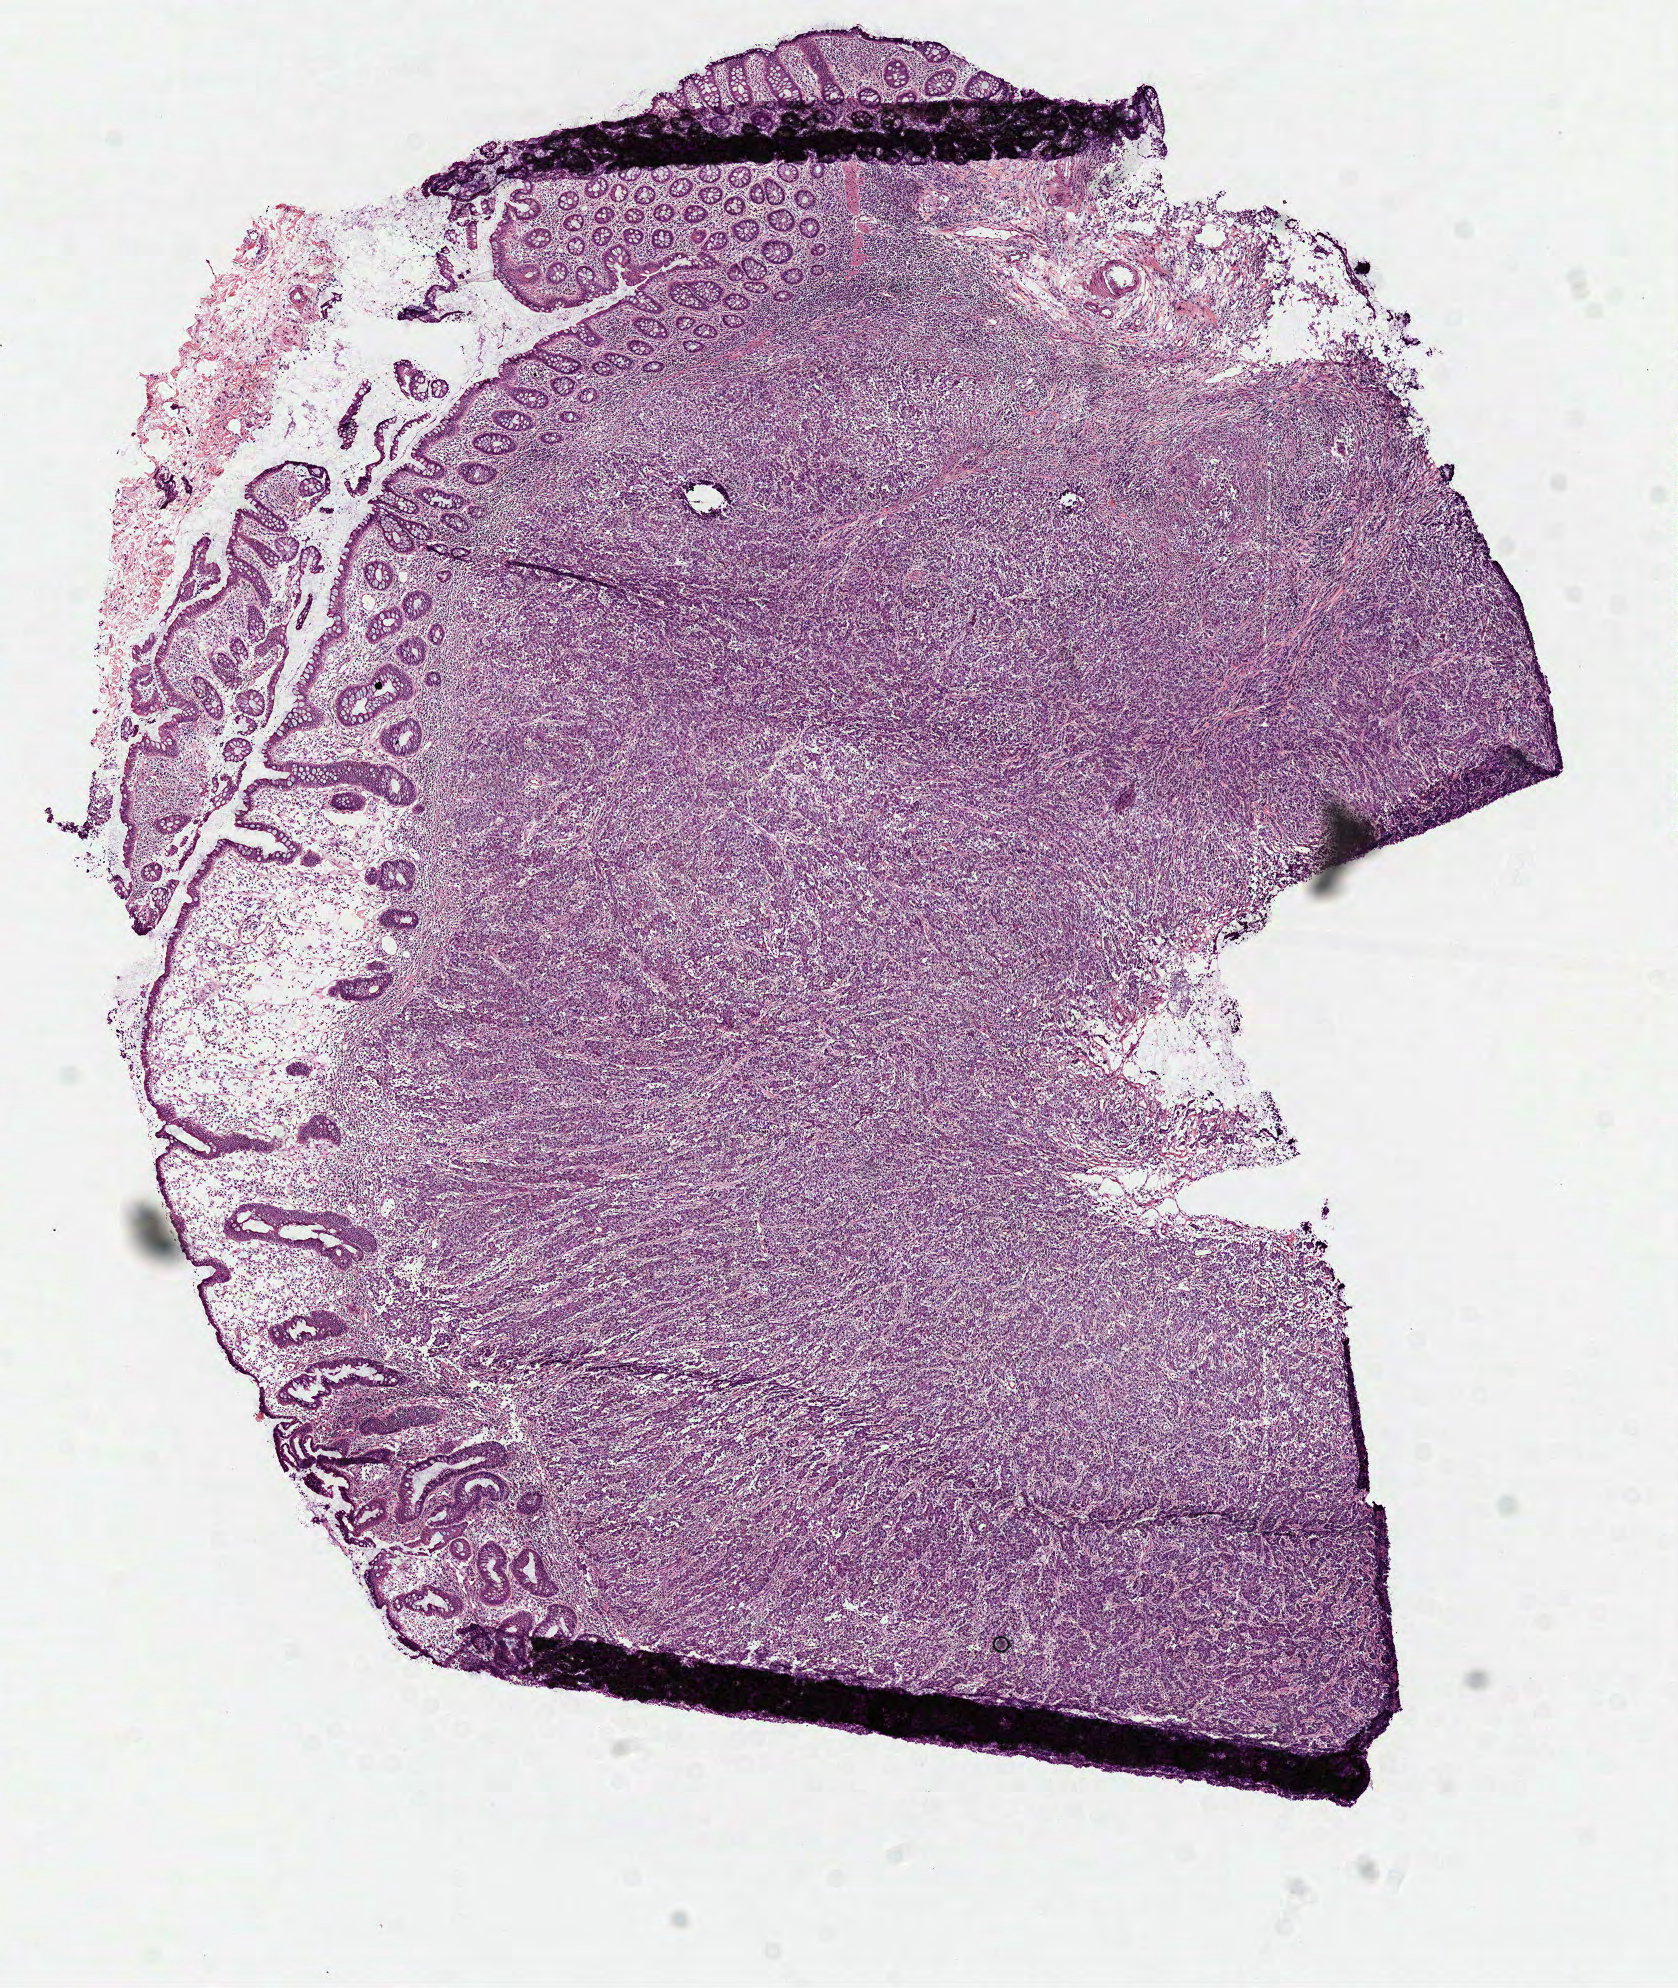
Digitized H&E tissue section (whole slide), low-resolution overview of the scanned area, about 6.8 x 8.0 mm. Frozen section from the top of the tissue portion. Colon, primary tumour sample. Patient: male, age at initial diagnosis 78 years. Pathologist review of this section (percent, as recorded): tumour cells 80%, tumour nuclei 75%, normal cells 10%, stromal cells 10%, necrosis 0%.
- lymph nodes positive (case pathology): 0 of 16 examined
- diagnosis: Adenocarcinoma, NOS (cecum)
- AJCC pathologic stage: I